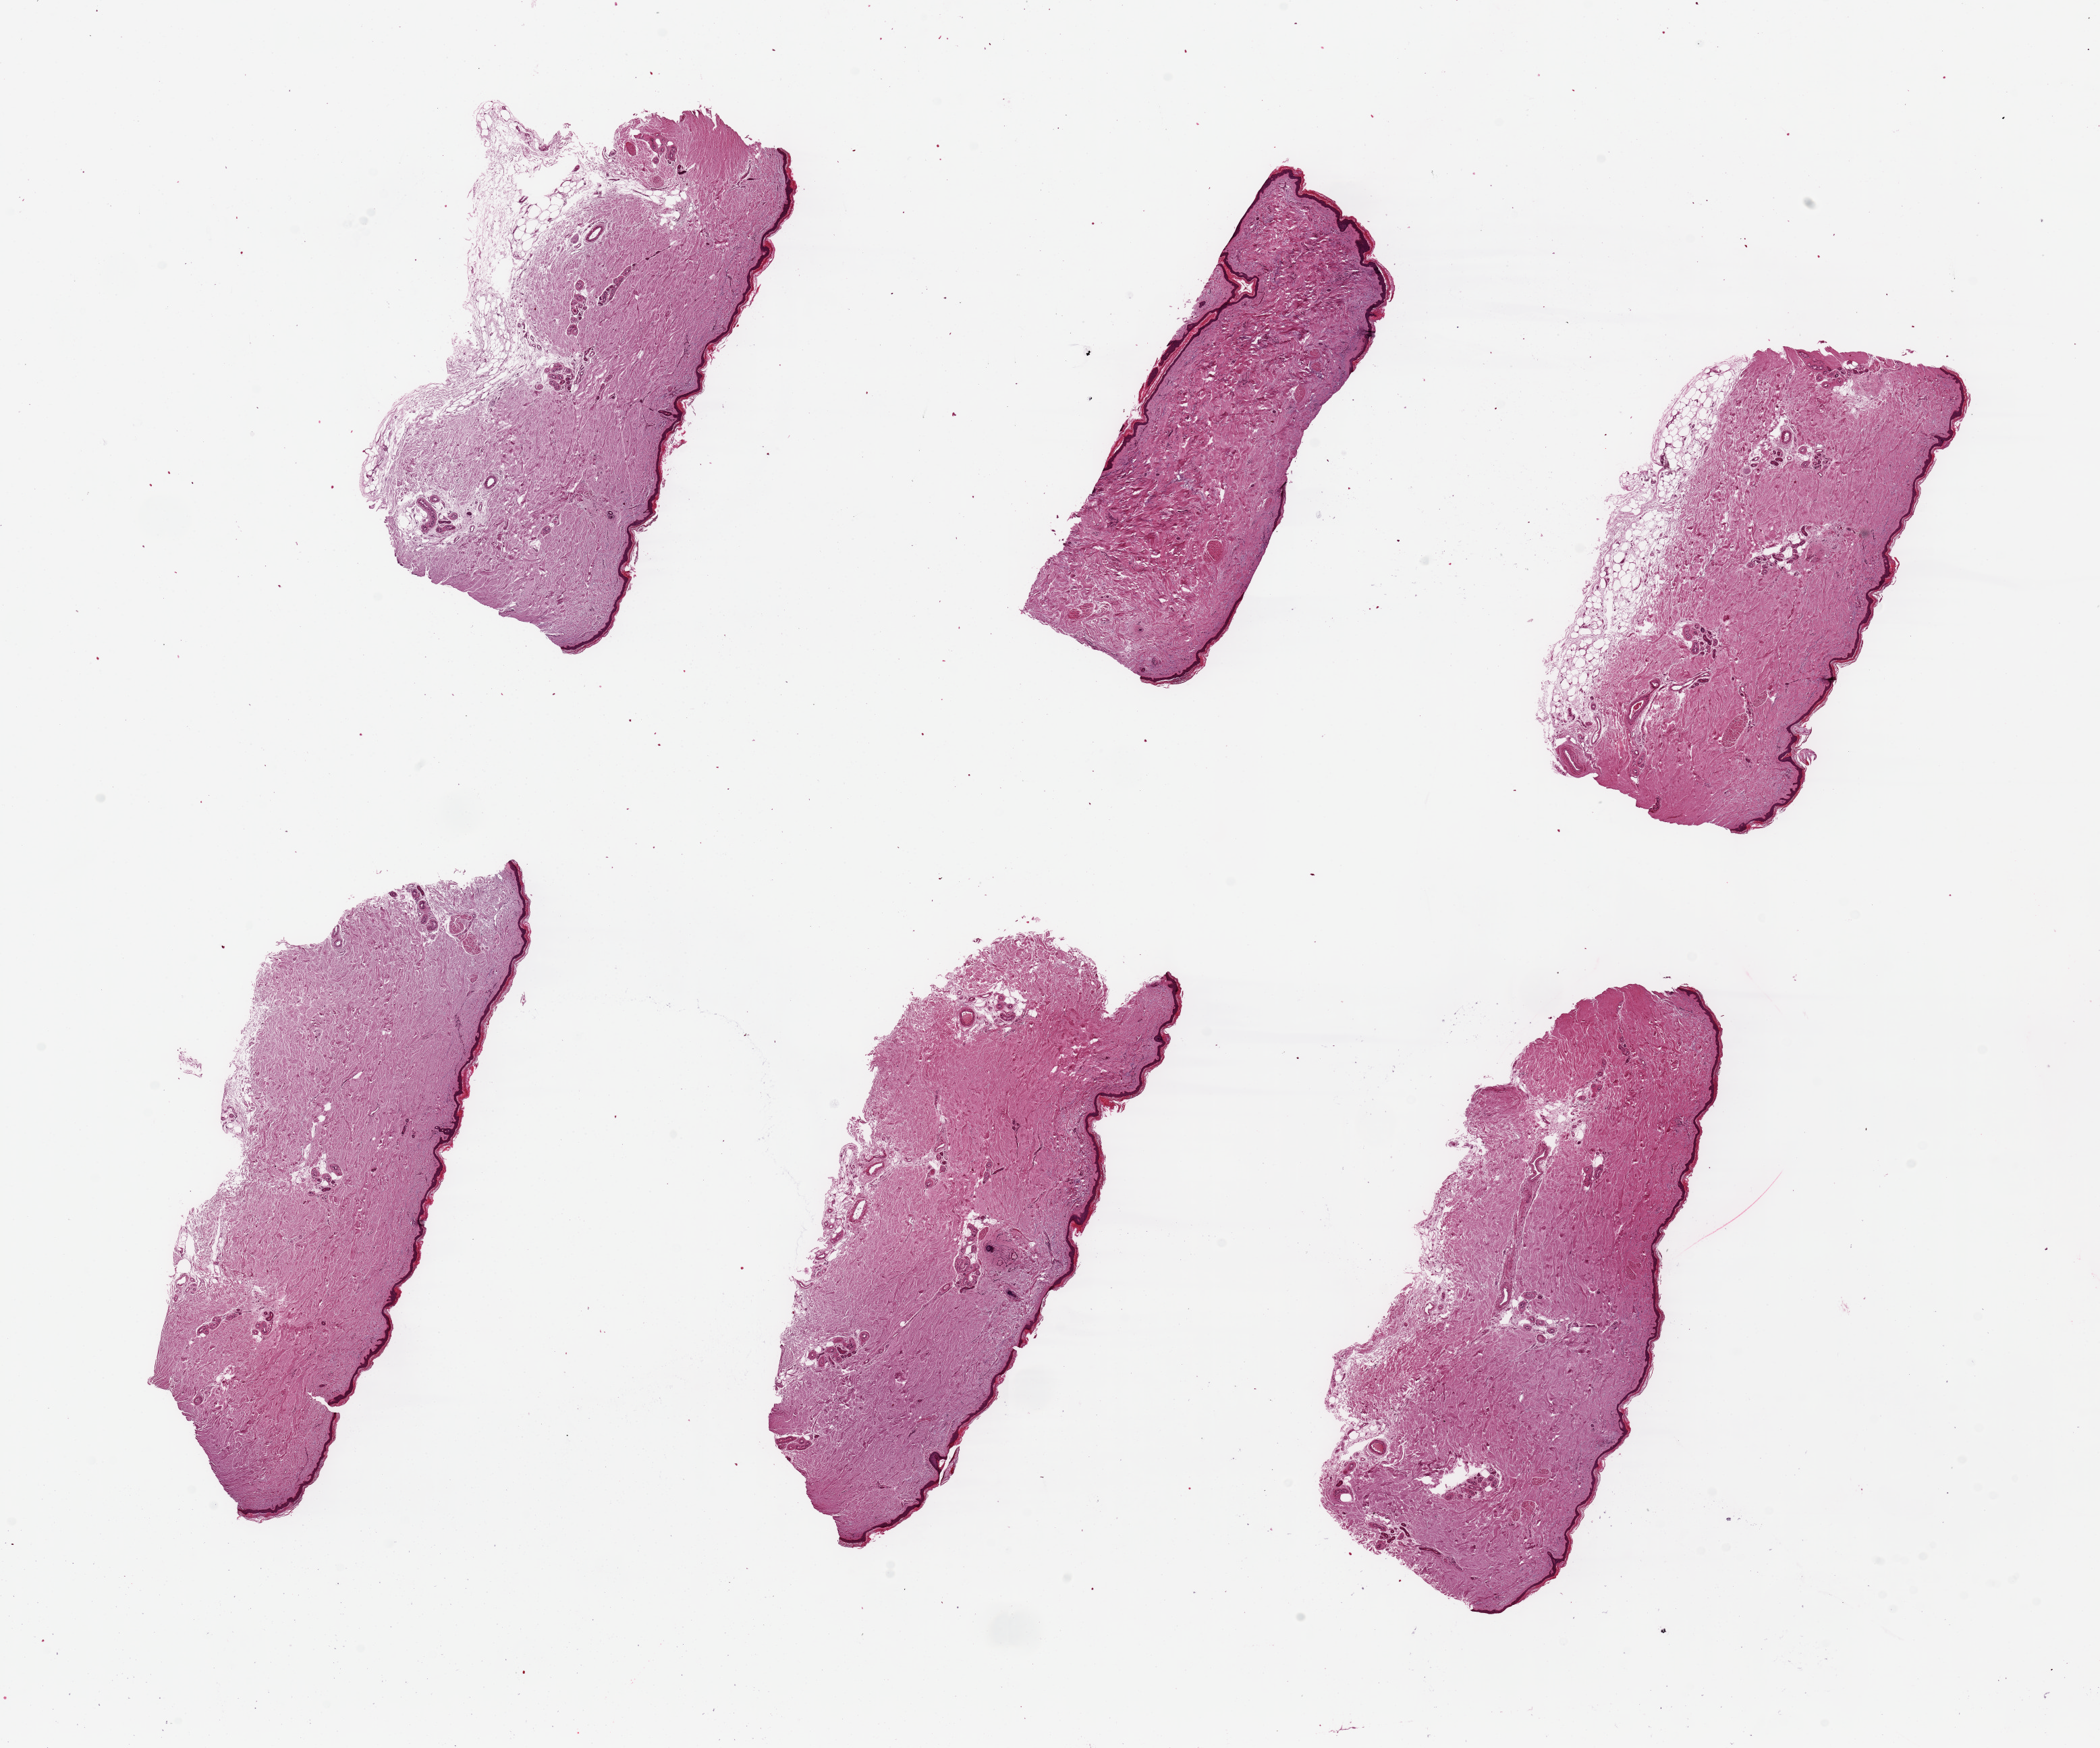
Whole-slide image, haematoxylin and eosin stain, a low-resolution overview of the entire scanned area, about 24.6 x 20.5 mm, PAXgene-fixed paraffin-embedded (PFPE) section, target tissue: skin of lower leg, tissue donor sample.
Reviewer comment on this tissue sample: 6 pieces, up to 6x3.5mm; subcutaneous adipose up to 0.7mm on 2 pieces.